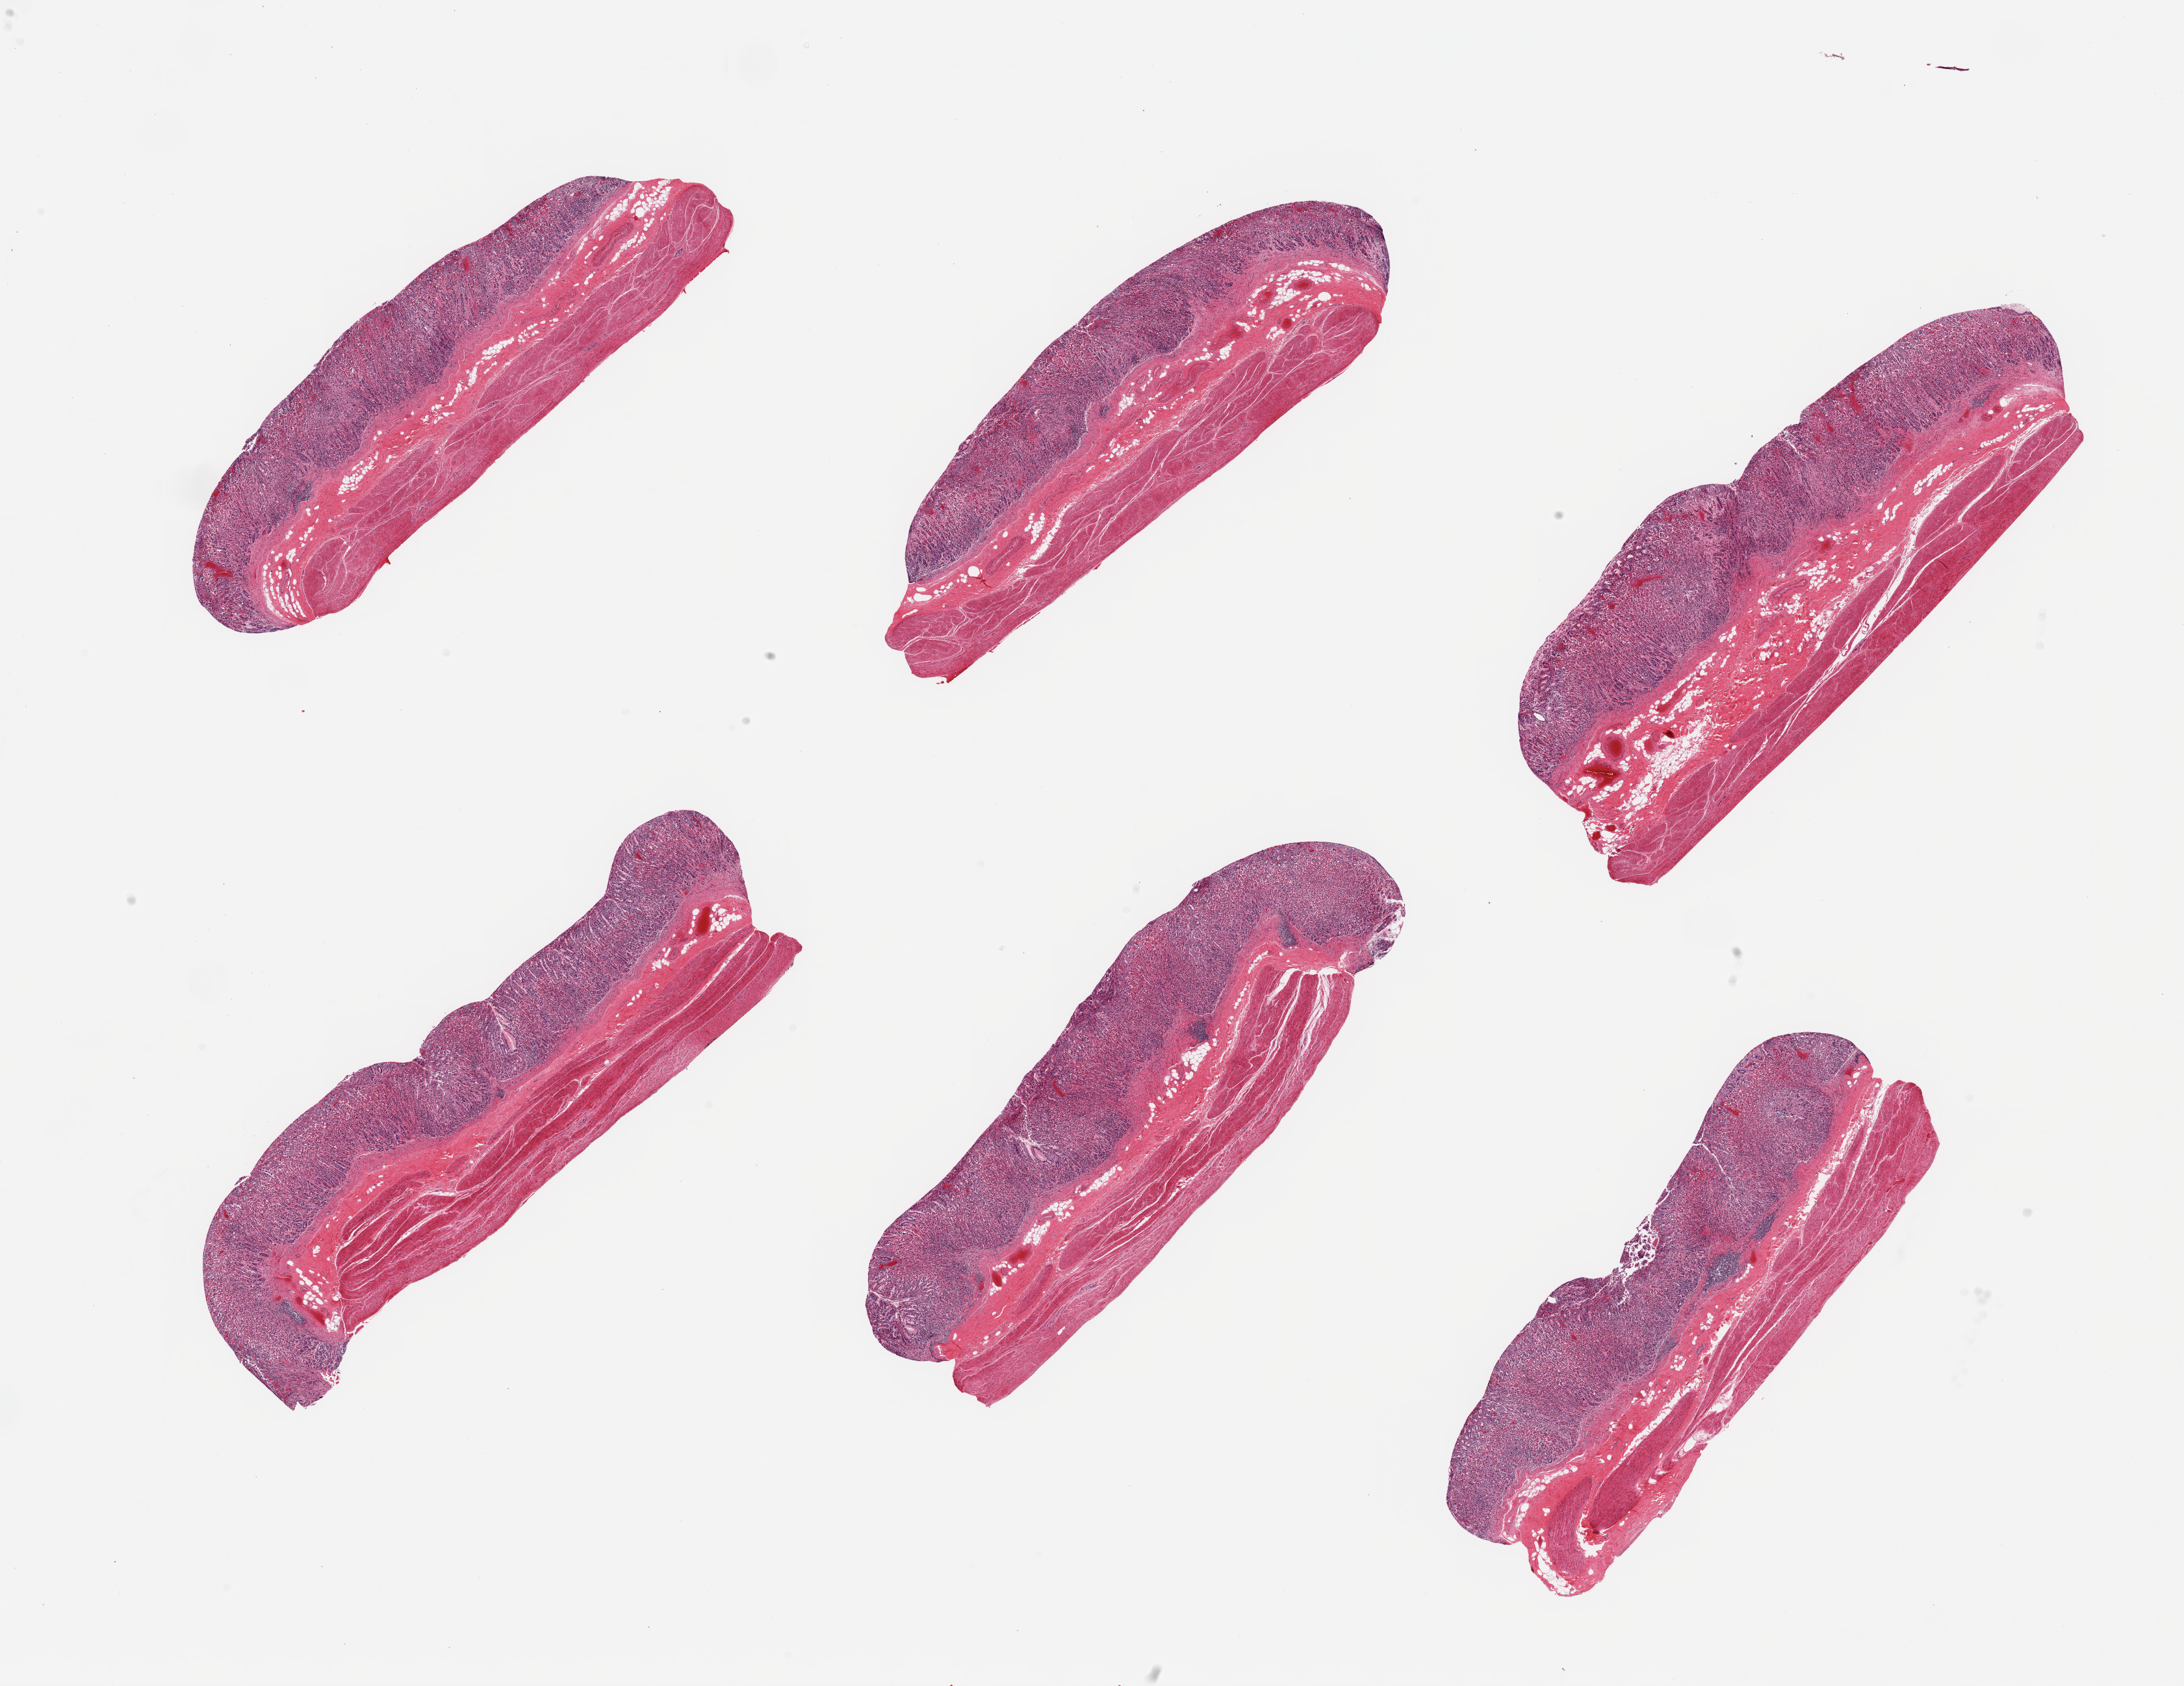
Hematoxylin and eosin (H&E) whole-slide image, brightfield — shown as a low-resolution overview of the whole scanned area (about 26.6 x 20.5 mm). PAXgene-fixed, paraffin-embedded tissue. Section of stomach (target tissue). Tissue donor sample.
Pathologist's review note for this sample: 6 pieces; chronic gastritis; muscularis better preserved [1] than mucosa.